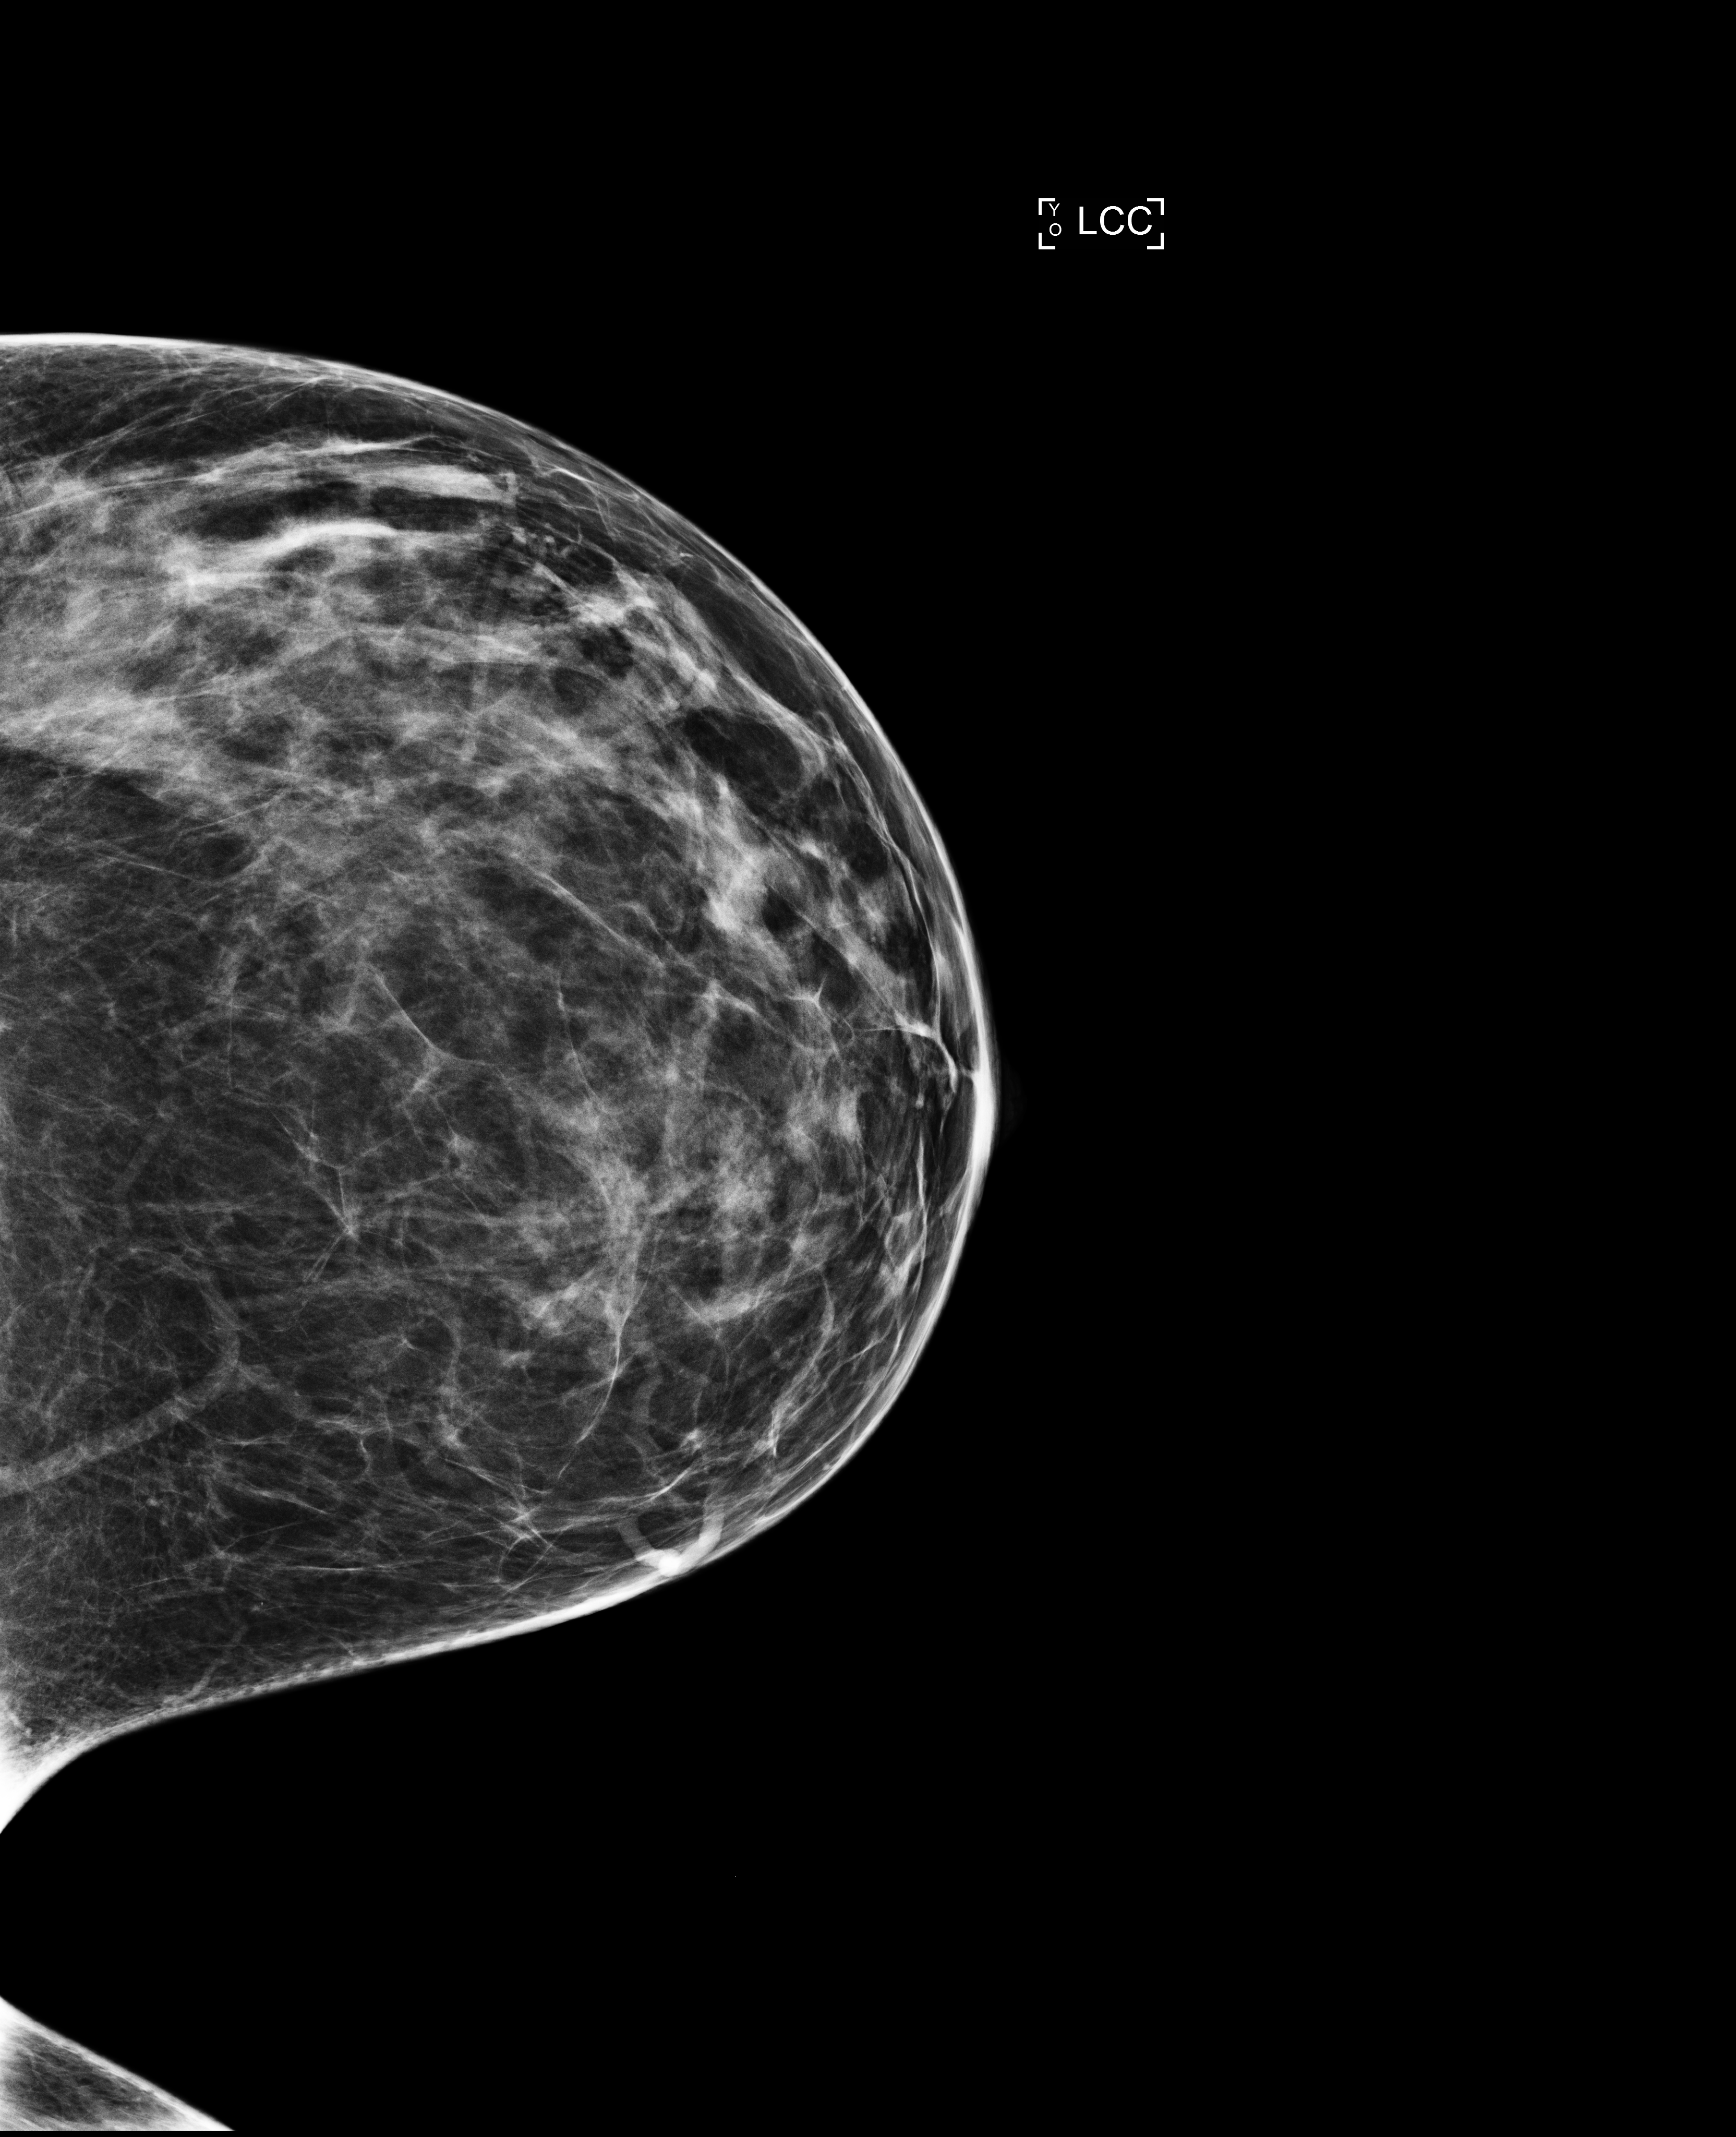
Screening examination; compressed breast thickness 71 mm; system: Selenia Dimensions. Patient: female, 43 years.
Image type: full-field digital mammogram. Breast: left. Projection: CC view.